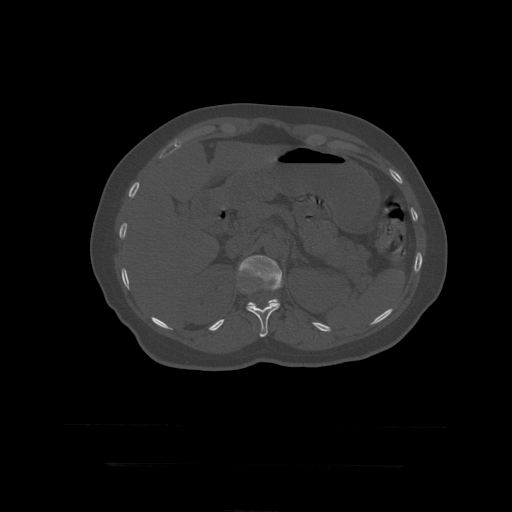
CT including the spine, one axial slice; position 189 of 399 along the scan axis; 120 kVp; bone window (W 1800 / L 400 HU); 512 × 512 image matrix. Patient age 41 years. From the clinical record (not read from this slice): primary cancer: breast.
Outlined on this slice (semi-automatically segmented with operator editing):
- L1 vertebra: bounding box [x1, y1, x2, y2] px = [239, 256, 283, 307]
- T12 vertebra: [242, 269, 280, 337]